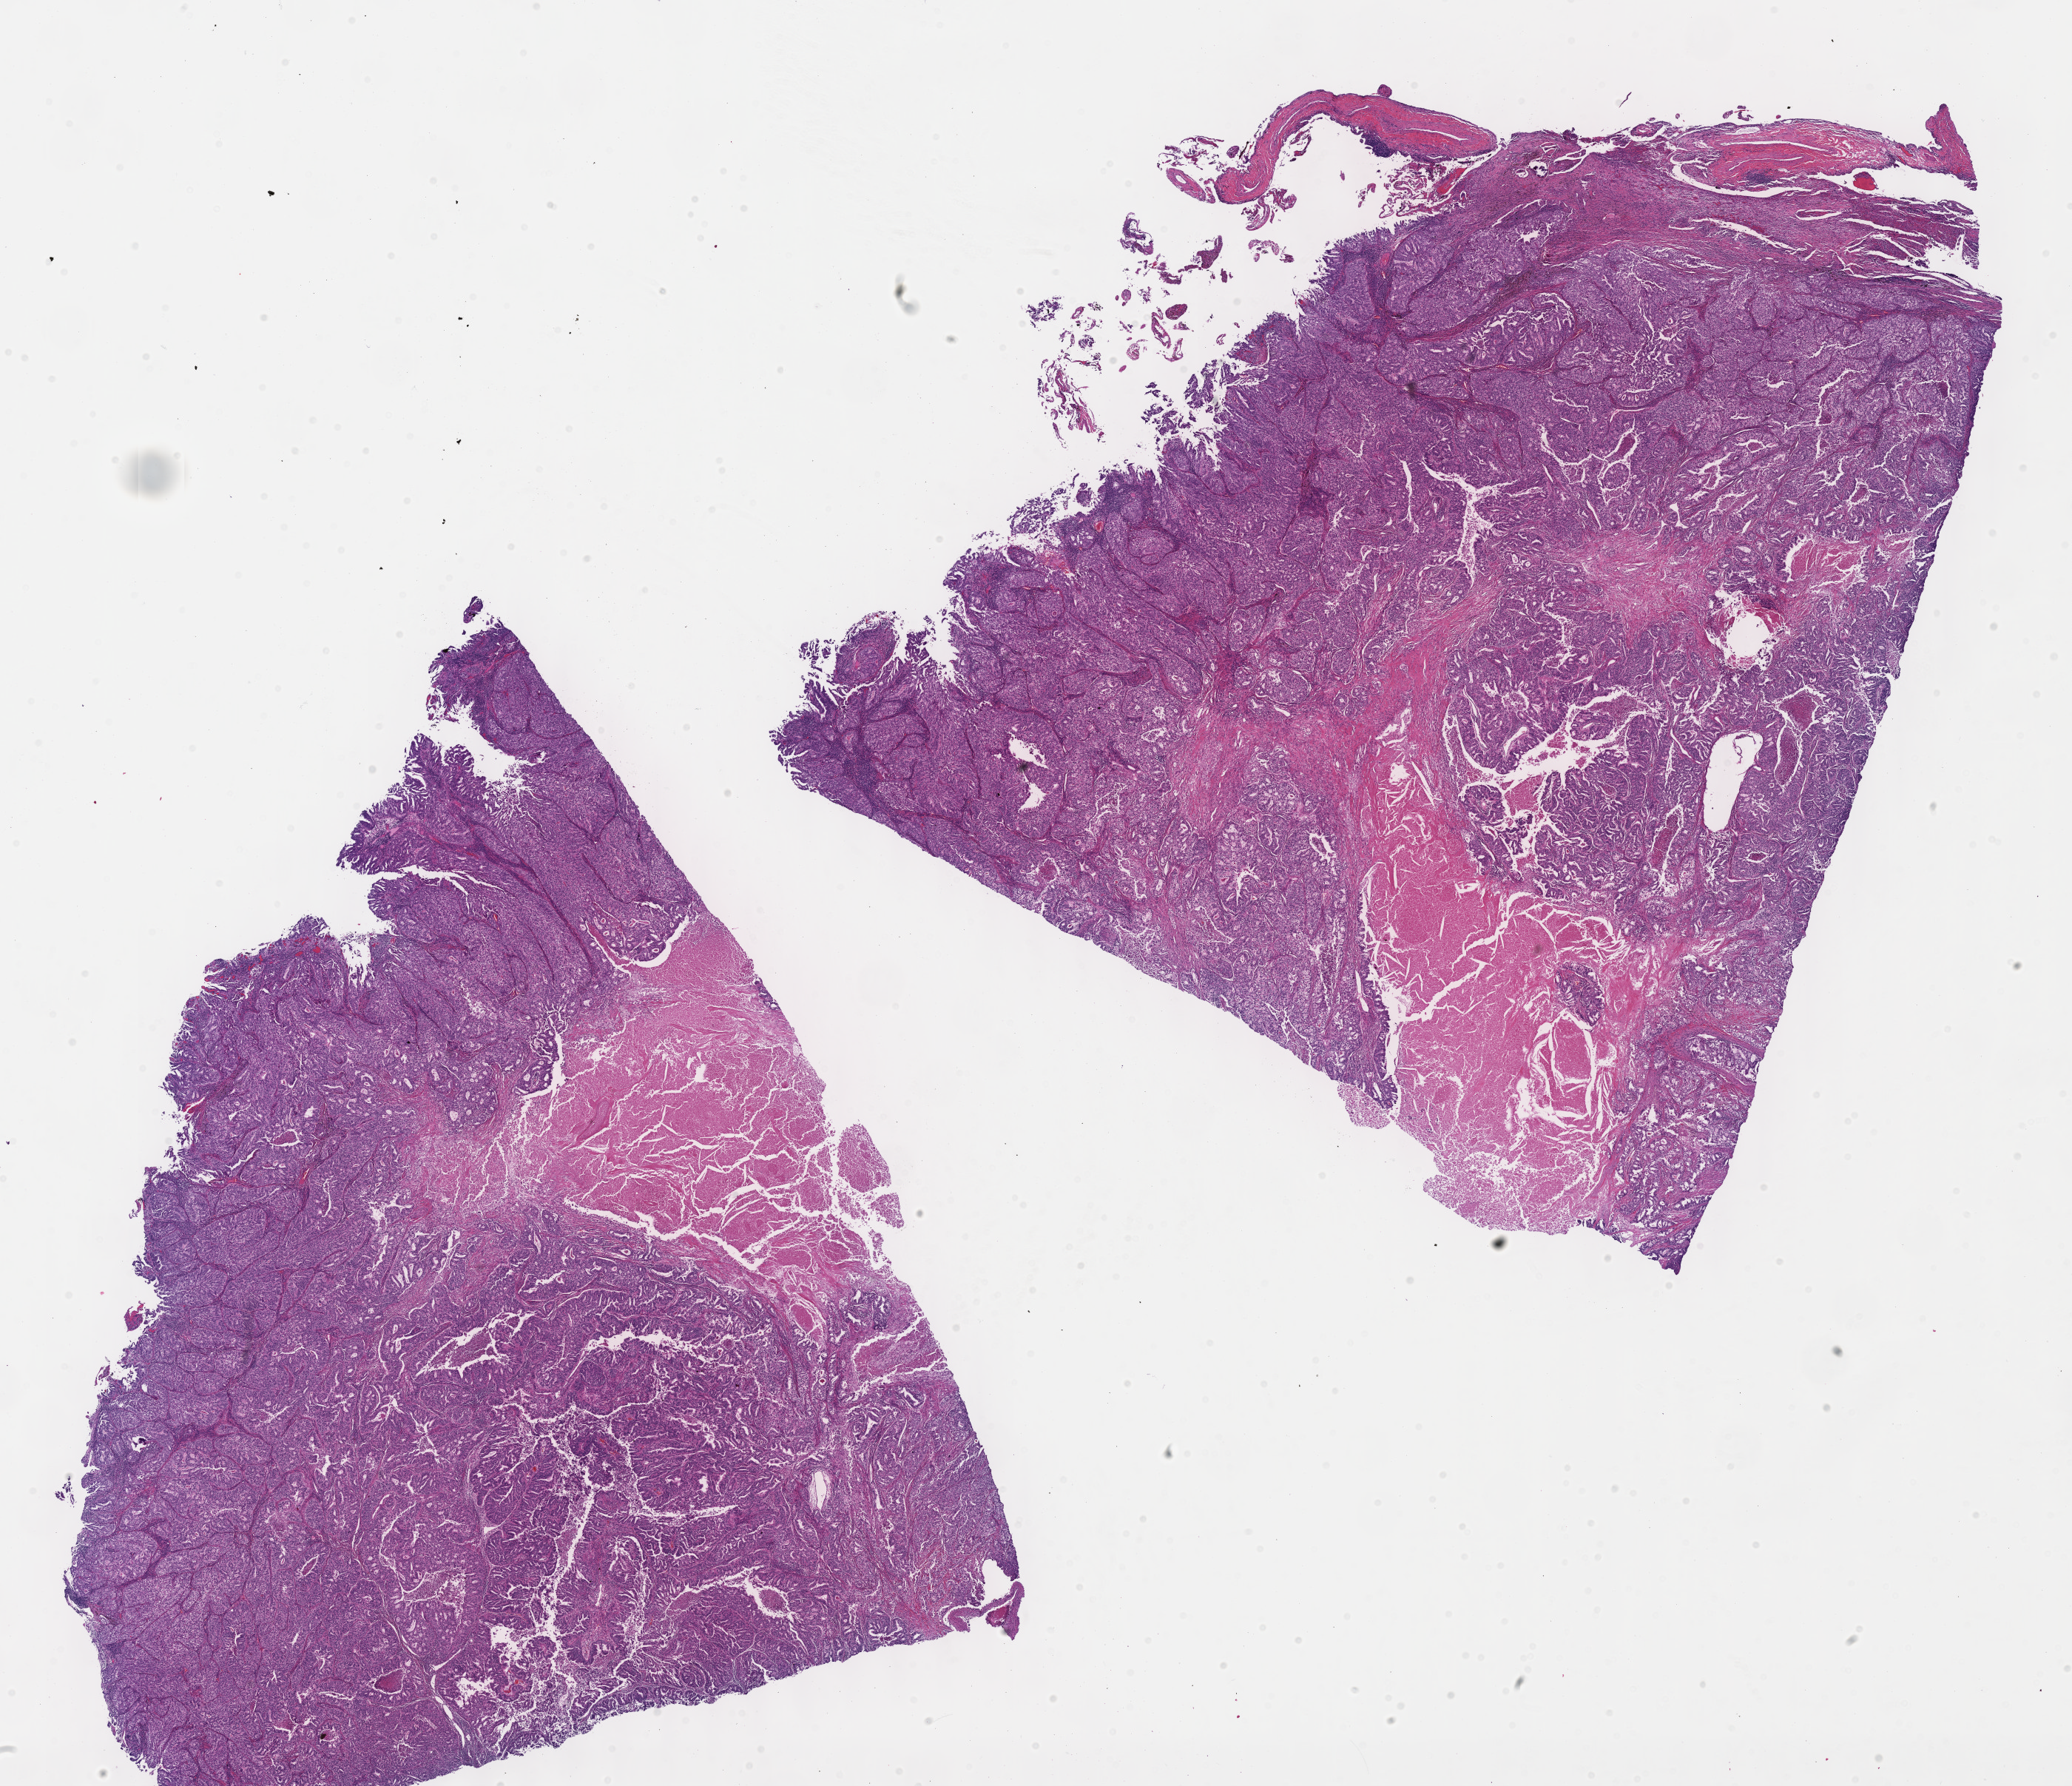
Whole-slide histology image, Hematoxylin and eosin (H&E) stained, low-resolution overview of the scanned area, about 22.6 x 19.5 mm (acquisition: 40x scan). Formalin-fixed paraffin-embedded (FFPE) diagnostic section. Lung, primary tumour sample. Patient: female, age at initial diagnosis 41 years.
Diagnosis: Adenocarcinoma, NOS (upper lobe, lung).